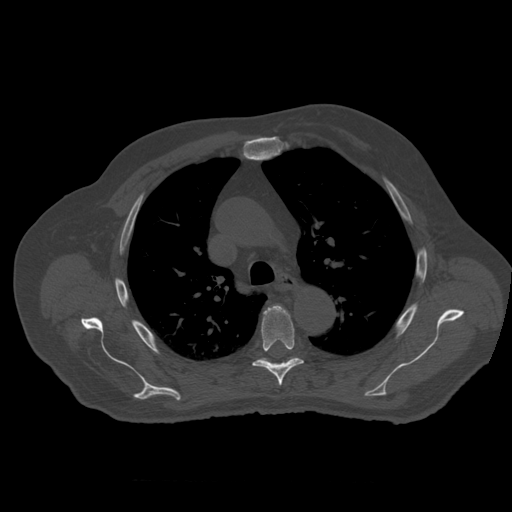
CT including the spine, one axial slice; slice 399 of 399 in the series (ordered by position); reconstruction kernel STANDARD; 120 kVp; bone window (W 1800 / L 400 HU); 1.25 mm slice thickness; 512 × 512 image matrix, field of view 407 × 407 mm. Patient age 73 years. From the clinical record (not read from this slice): primary cancer: prostate; vertebrae with lytic lesions (as recorded): L2.
Structures marked on this image (semi-automatic segmentation, software-assisted and operator-edited):
- T5 vertebra: box from (x=254, y=305) to (x=304, y=387) px
- T6 vertebra: (x=258, y=357)–(x=298, y=363)